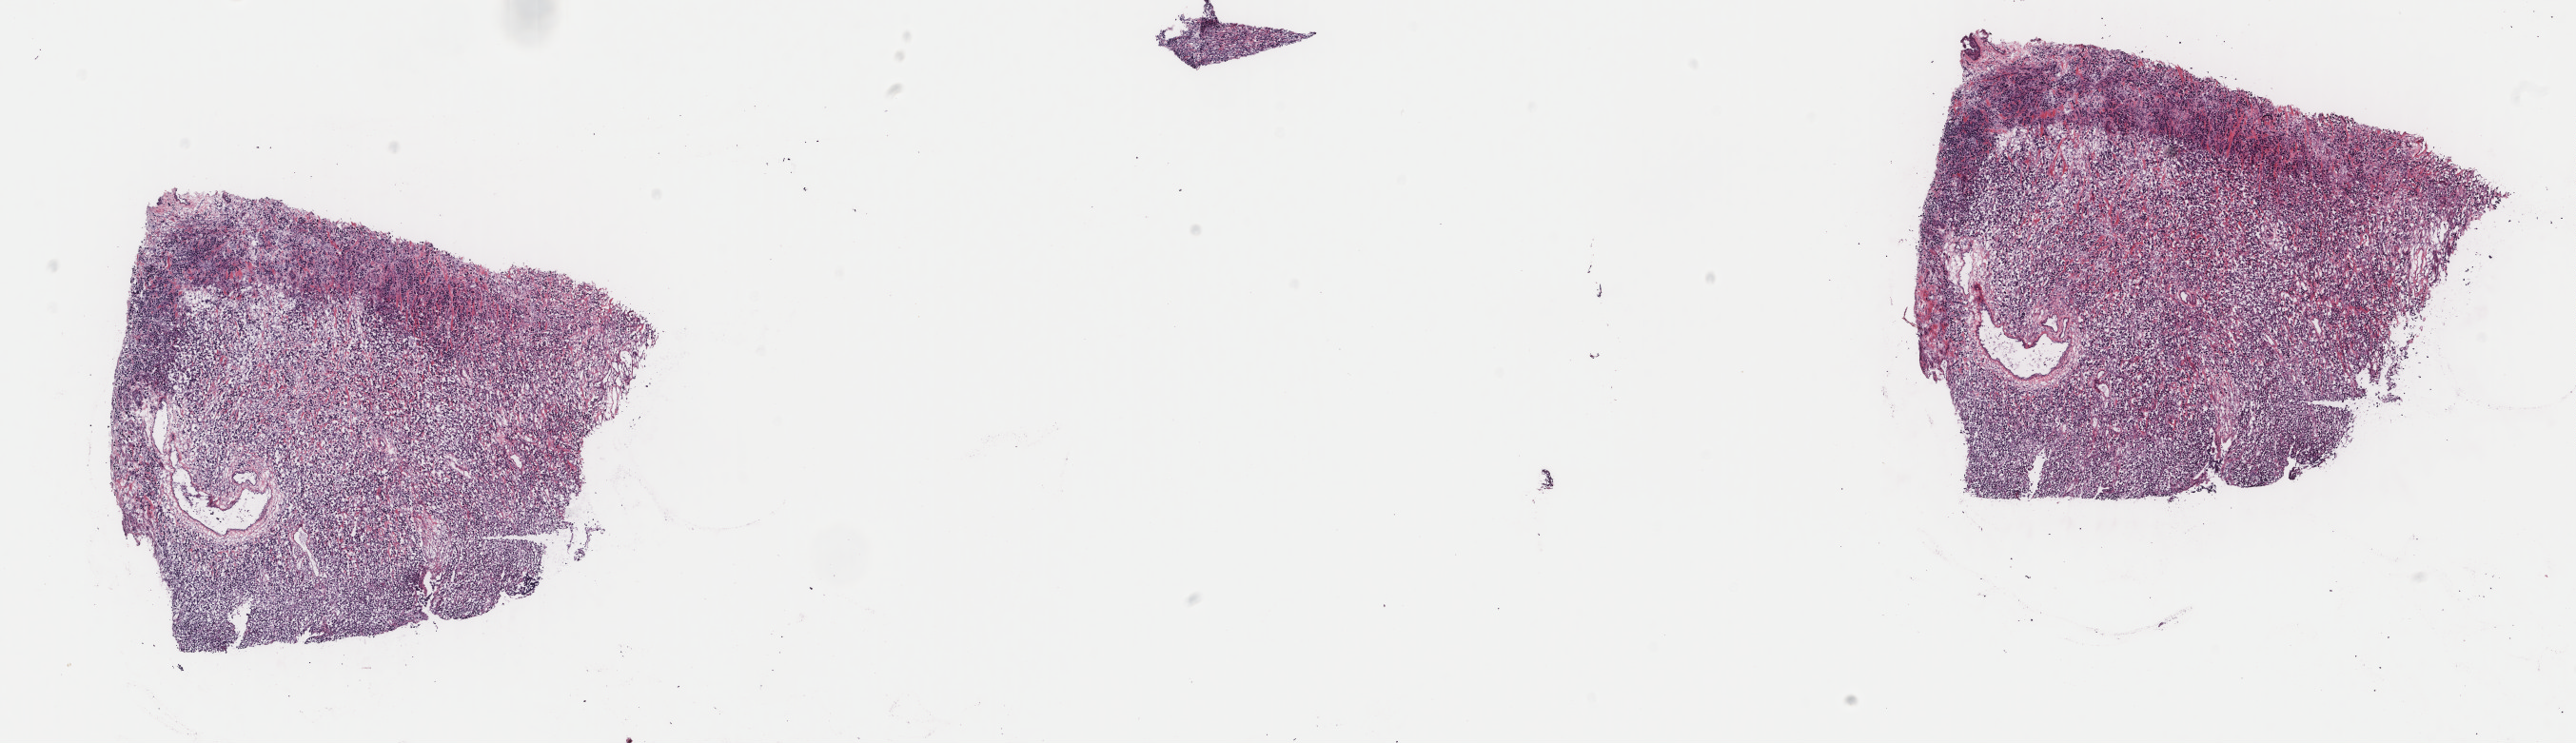
Whole-slide histology image, H&E — a low-resolution overview of the entire scanned area, about 21.5 x 6.2 mm; frozen section from the top of the tissue portion; bladder, primary tumour sample. Female patient; age at initial diagnosis 87 years. Histologic grade: high grade. Composition of this section per pathologist review: tumour cells 75%, tumour nuclei 75%, normal cells 0%, stromal cells 25%, necrosis 0%. Inflammatory infiltration, as recorded: lymphocyte infiltration 5%, monocyte infiltration 0%, neutrophil infiltration 0%.
* AJCC pathologic stage: III (7th edition)
* TNM: T4a NX MX
* pathologic diagnosis: Transitional cell carcinoma (posterior wall of bladder)